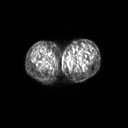
FDG PET of an extremity soft-tissue mass (from a PET/CT study), one axial slice; 3.27 mm slice thickness; 128 × 128 image matrix. Patient: female, 24 years. From the clinical record (not read from this slice): histological type: leiomyosarcoma; grade: high; site of the primary tumour: groin.
Annotated regions visible in this slice (expert contour drawn on MRI and transferred to this co-registered scan by the dataset authors):
- gross tumour volume including surrounding oedema: bounding box <62,57,69,62> (left, top, right, bottom; pixels)